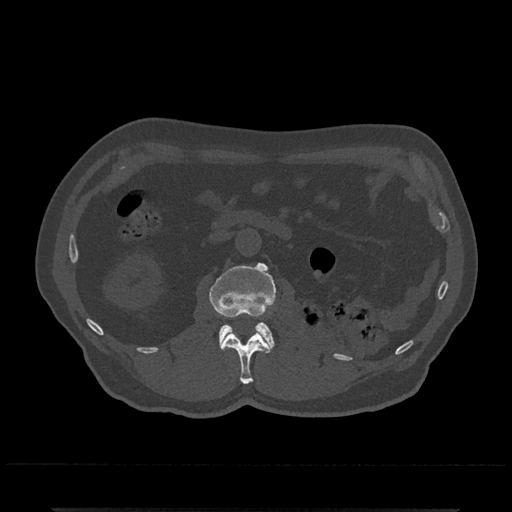
CT including the spine, one axial slice; position 325 of 797 along the scan axis; bone window (W 1800 / L 400 HU); 0.5 mm slice thickness; 512 × 512 image matrix, field of view 393 × 393 mm. Patient: male, 67 years. From the clinical record (not read from this slice): primary cancer: prostate.
Structures marked on this image (semi-automatically segmented with operator editing):
- L1 vertebra: bounding box <221,331,270,385> (left, top, right, bottom; pixels)
- L2 vertebra: <210,262,277,351>